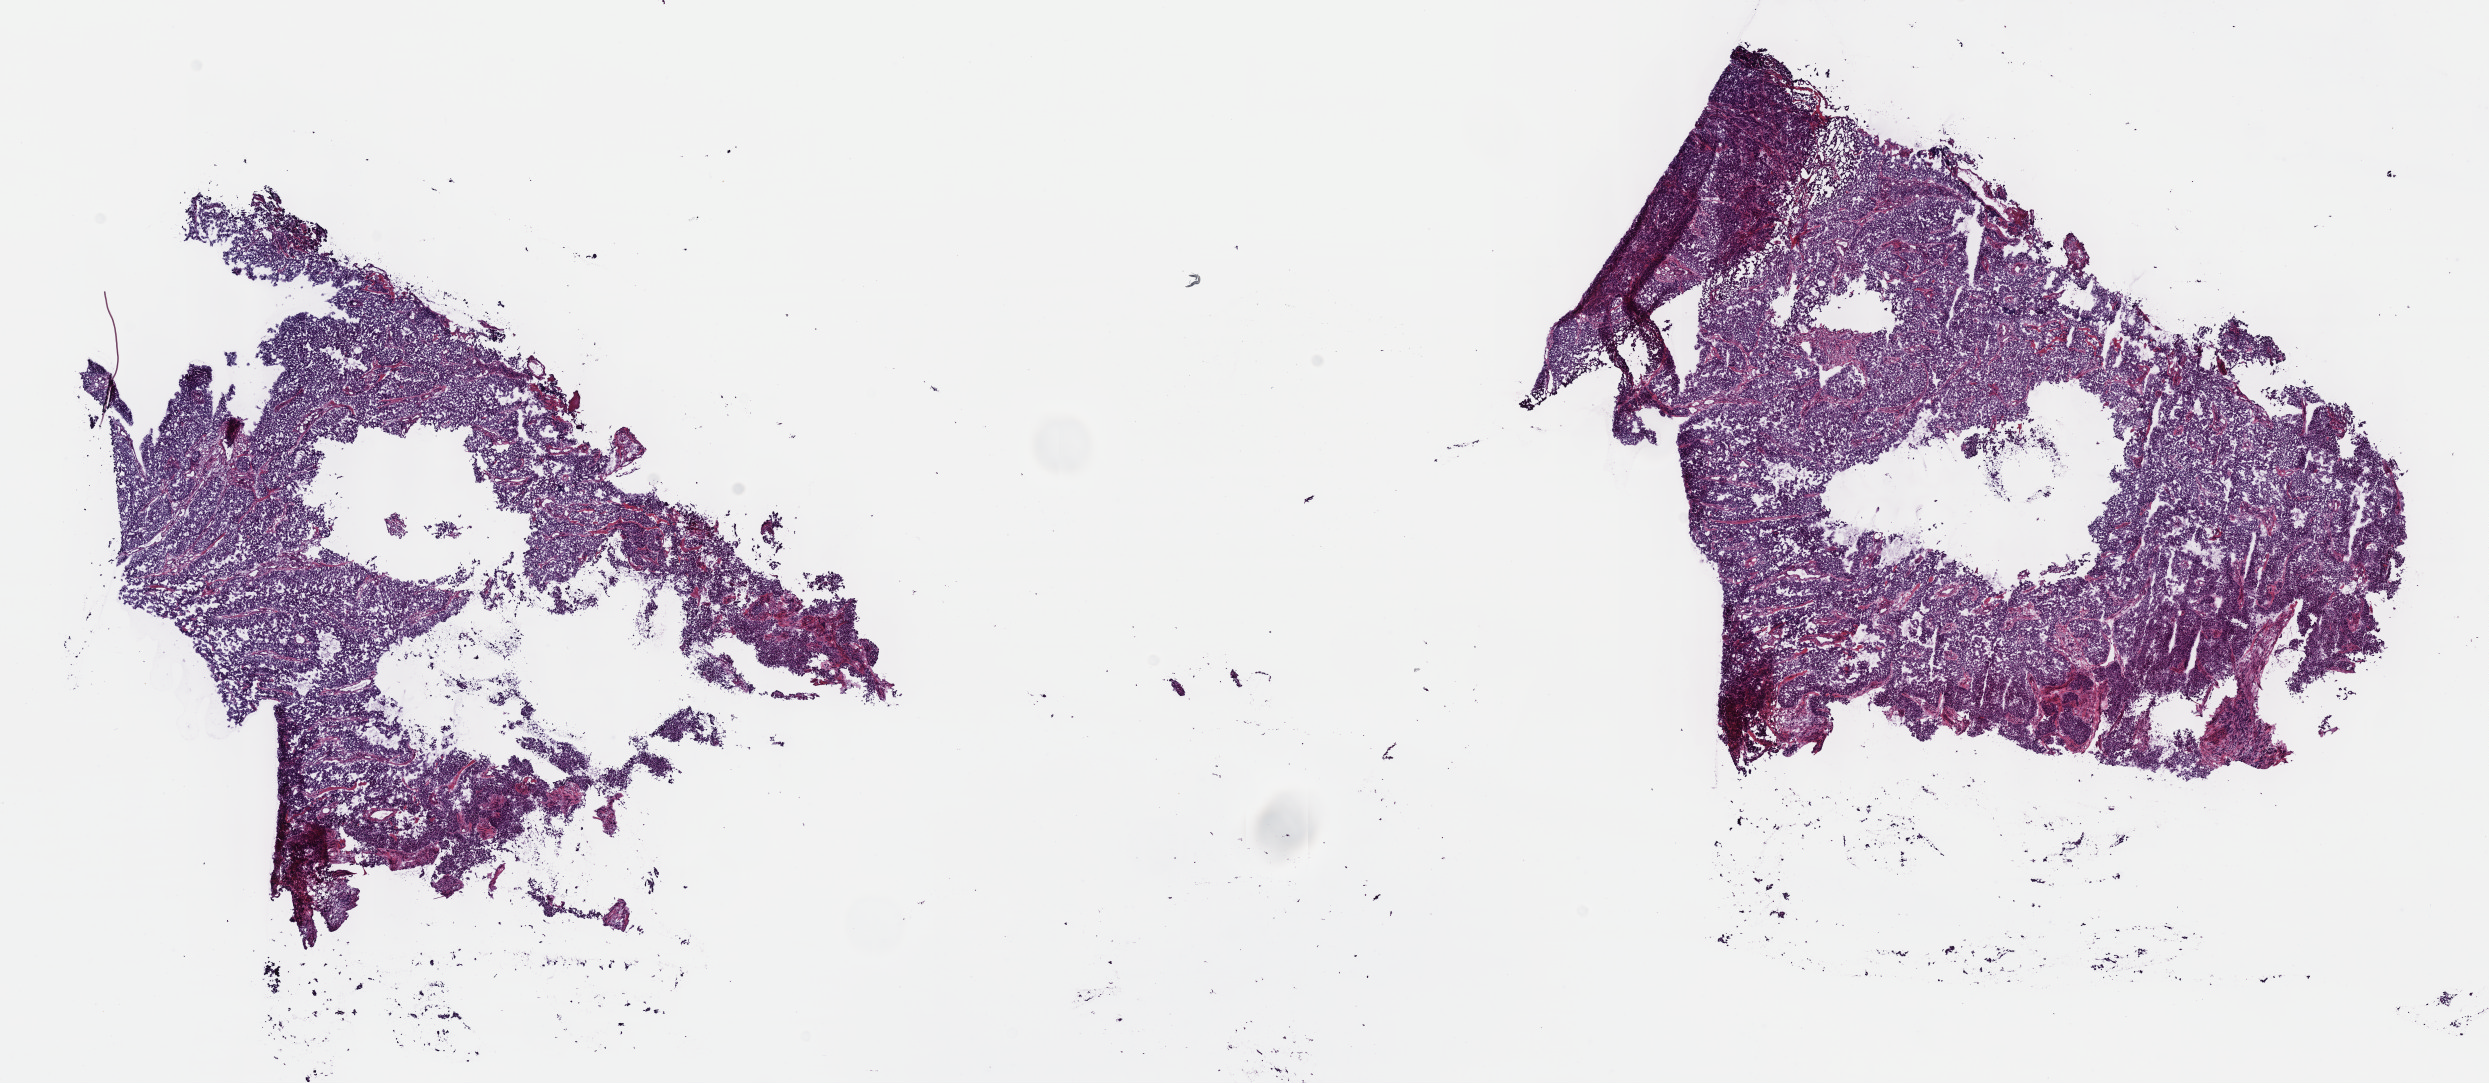
H&E whole-slide image, shown as a low-resolution overview of the whole scanned area (about 20.1 x 8.8 mm, slide scanned at 40x), frozen section from the top of the tissue portion, primary tumour sample from the bladder. Patient: male, age at initial diagnosis 73 years. Histologic grade: high grade. Composition of this section per pathologist review: tumour cells 100%, tumour nuclei 75%, normal cells 0%, stromal cells 0%, necrosis 0%. Inflammatory infiltration, as recorded: lymphocyte infiltration 2%, monocyte infiltration 0%, neutrophil infiltration 0%.
Diagnosis: Papillary transitional cell carcinoma (trigone of bladder). AJCC pathologic stage: IV (7th edition). TNM: T4b N0 M0.